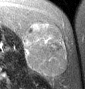
MRI of an extremity soft-tissue mass, one axial slice; position 18 of 46 along the scan axis; T2-weighted fat-saturated; MR volume resampled by the dataset authors to the PET/CT grid (not the native acquisition matrix); 3.27 mm slice thickness; 85 × 89 image matrix. Female patient. Case-level facts recorded for this patient, not image findings: histological type: leiomyosarcoma; grade: intermediate; site of the primary tumour: parascapusular.
Structures marked on this image (expert contour drawn on MRI and transferred to this co-registered scan by the dataset authors):
- gross tumour volume including surrounding oedema: bounding box <24,23,69,77> (left, top, right, bottom; pixels)
- gross tumour volume (mass): <24,23,69,77>